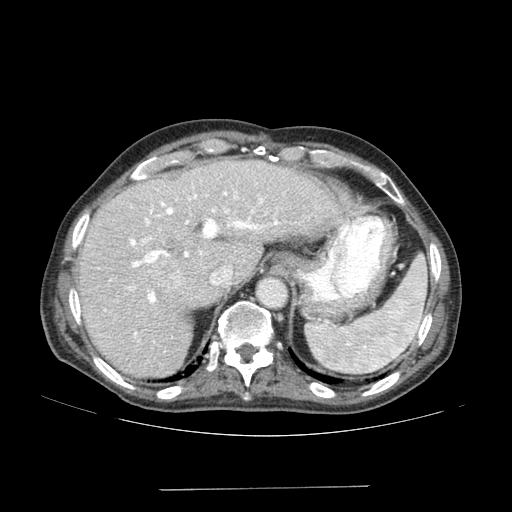
Contrast-enhanced abdominal CT (liver protocol), one axial slice; position 118 of 192 along the scan axis; soft-tissue window (W 400 / L 40 HU); 2.5 mm slice thickness; 512 × 512 image matrix, field of view 400 × 400 mm. From the clinical record (not read from this slice): diagnosis: hepatocellular carcinoma (patient treated with transarterial chemoembolisation; whether this scan precedes or follows treatment is not stated here); TNM stage (as recorded): Stage-IVA; Child-Pugh class: A.
Annotated regions visible in this slice (semi-automatic segmentation, software-assisted and operator-edited):
- liver parenchyma outside the tumour (the mass and vessels are separate outlines, so this box may not span the whole liver): bounding box <78,158,352,376> (left, top, right, bottom; pixels)
- mass: <147,258,184,296>
- liver vessels: <104,192,279,336>